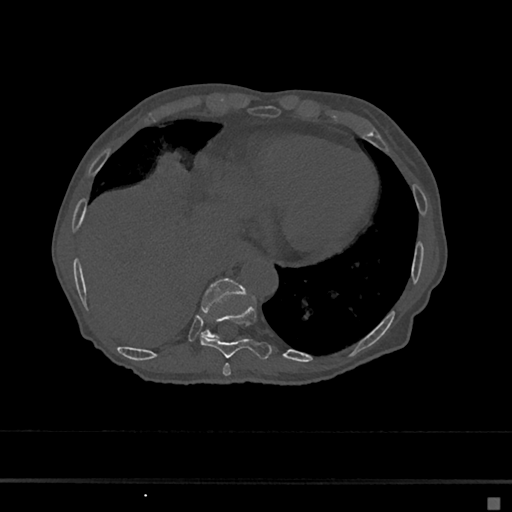
CT including the spine, one axial slice. Slice 262 of 797 in the series (ordered by position). Reconstruction kernel Br40s/3. 120 kVp. Bone window (W 1800 / L 400 HU). 0.5 mm slice thickness. 512 × 512 image matrix, field of view 360 × 360 mm. Patient: female, 68 years. Case-level facts recorded for this patient, not image findings: primary cancer: renal.
Outlined on this slice (semi-automatic segmentation, software-assisted and operator-edited):
- T10 vertebra: bounding box [x1, y1, x2, y2] px = [200, 278, 246, 339]
- T8 vertebra: [223, 363, 231, 376]
- T9 vertebra: [200, 304, 272, 360]